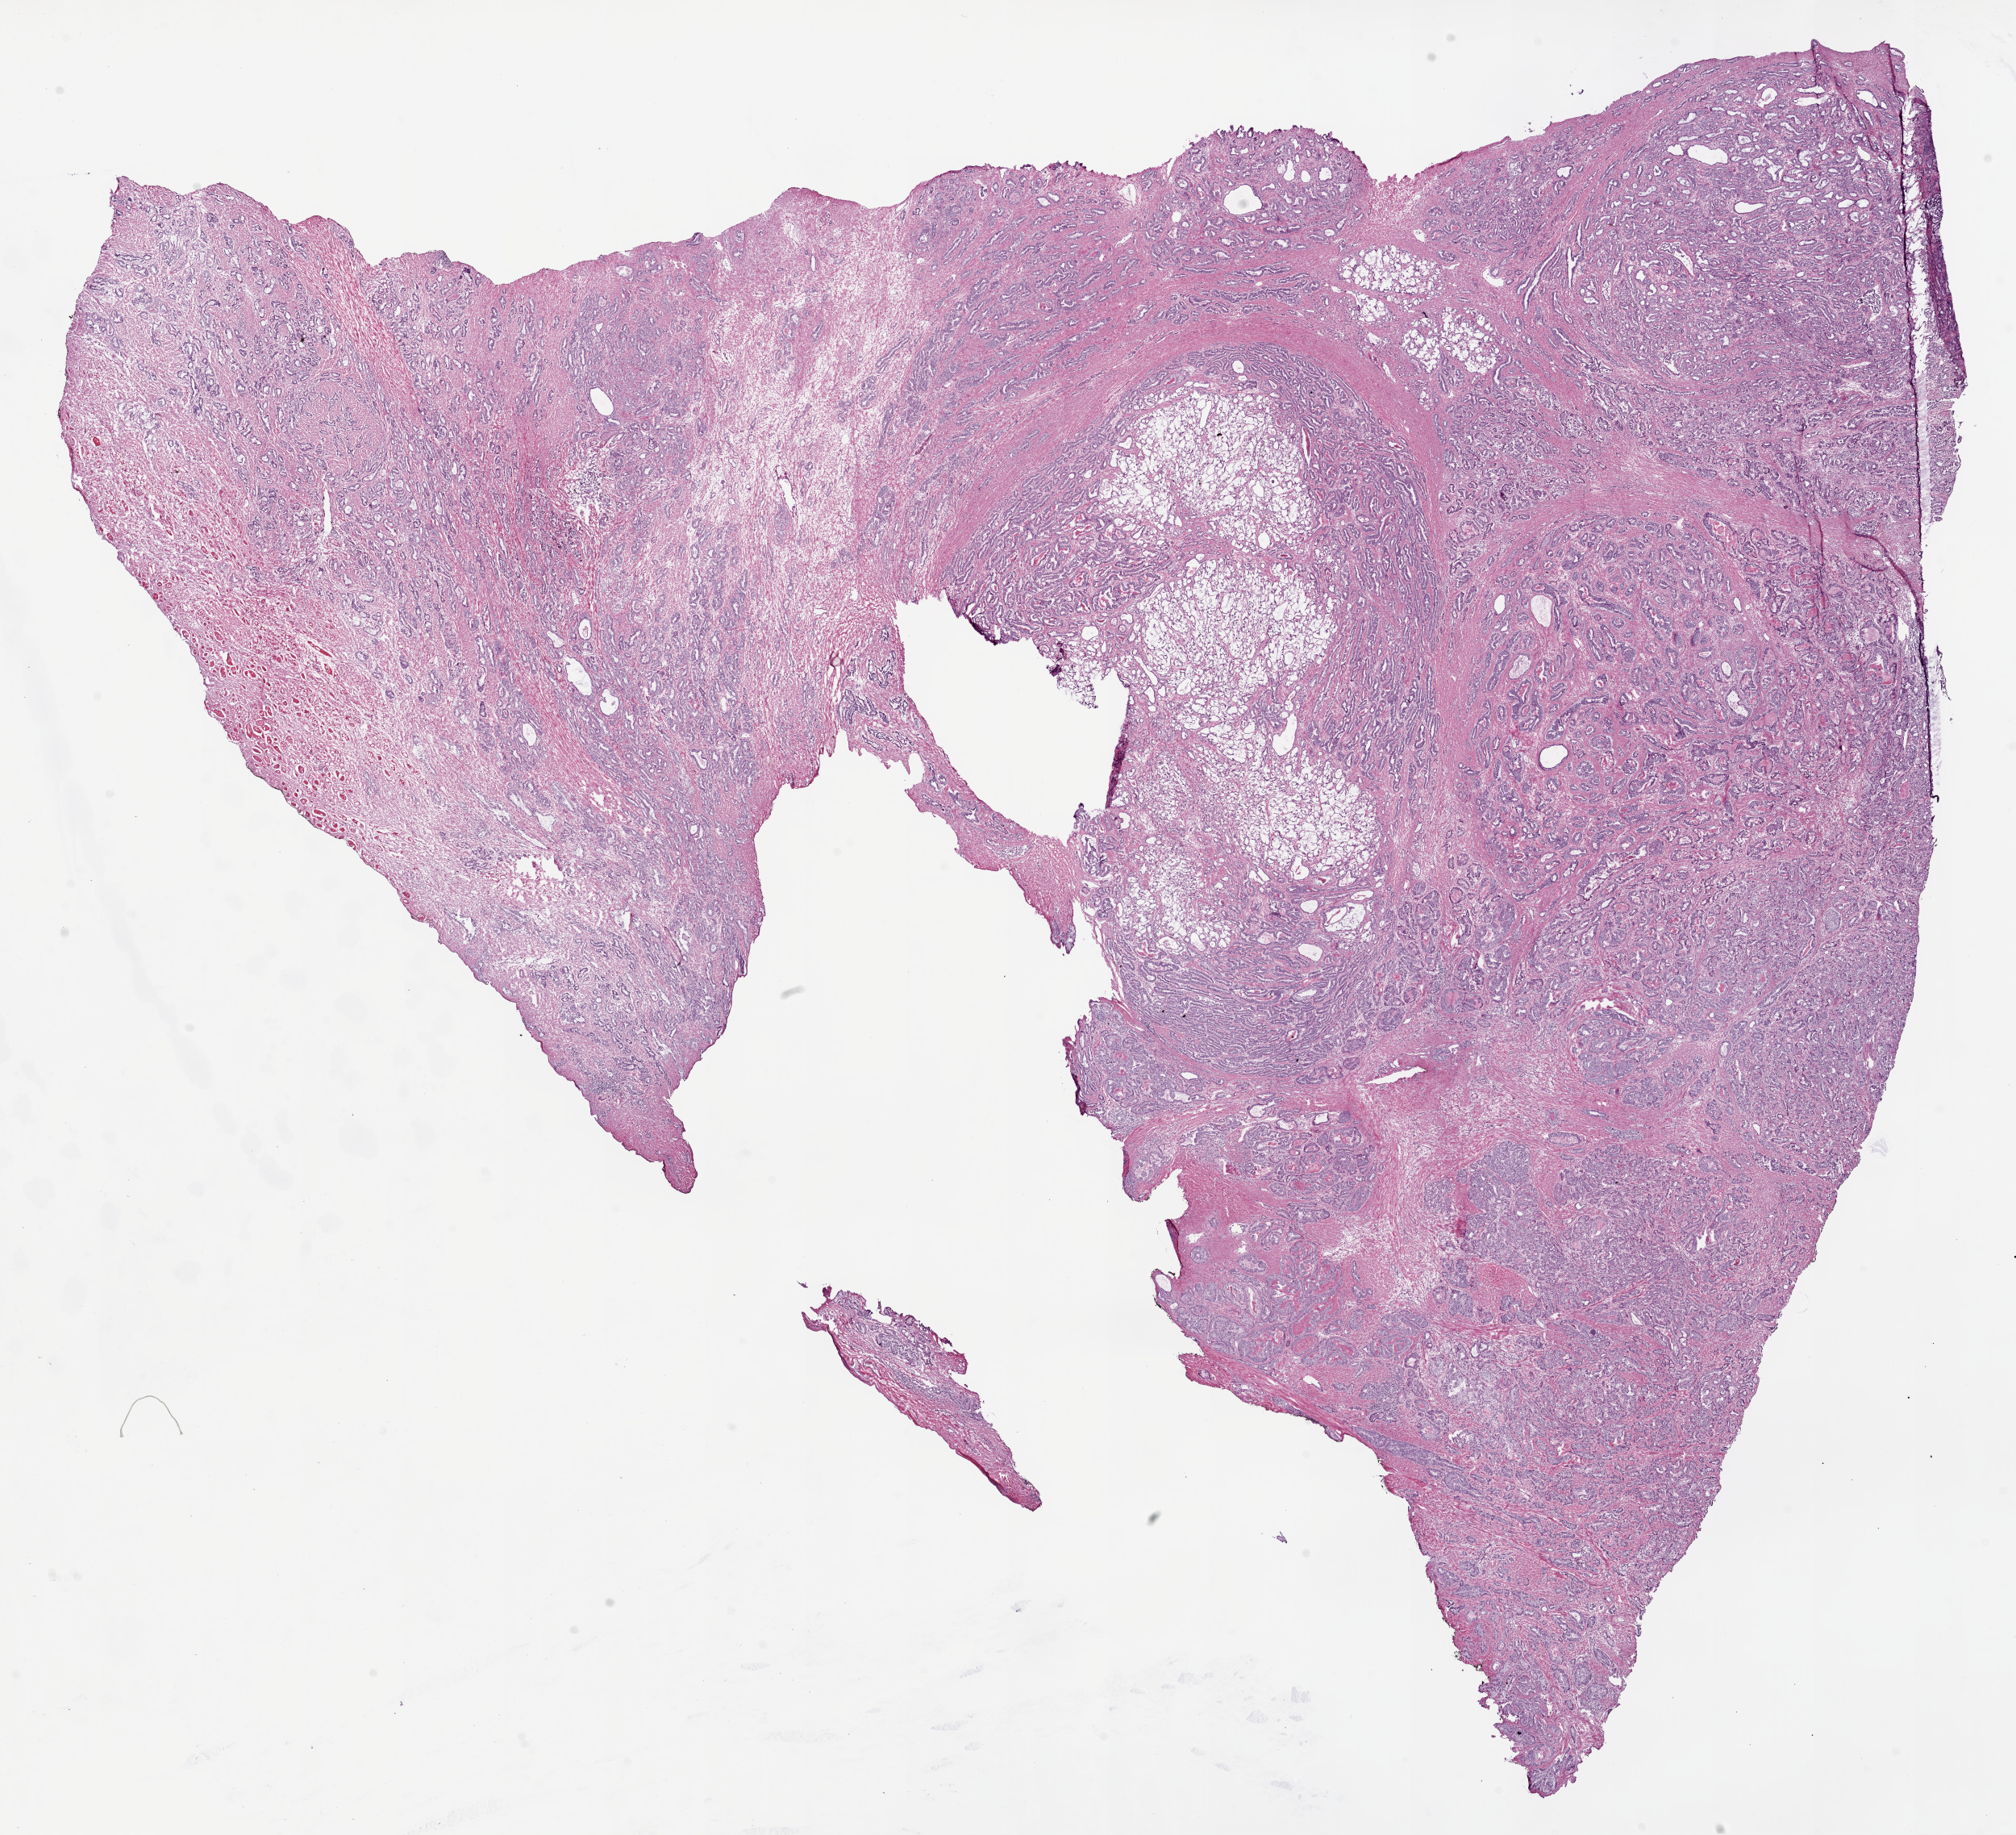
Whole-slide histology image, H&E-stained — low-resolution overview of the scanned area, about 20.1 x 18.3 mm. Frozen section from the top of the tissue portion. Sample: primary tumour, prostate. Patient: male, age at initial diagnosis 61 years. Slide review estimates, as recorded: tumour cells 70%, tumour nuclei 70%.
Histologic diagnosis: Acinar cell carcinoma (prostate gland).